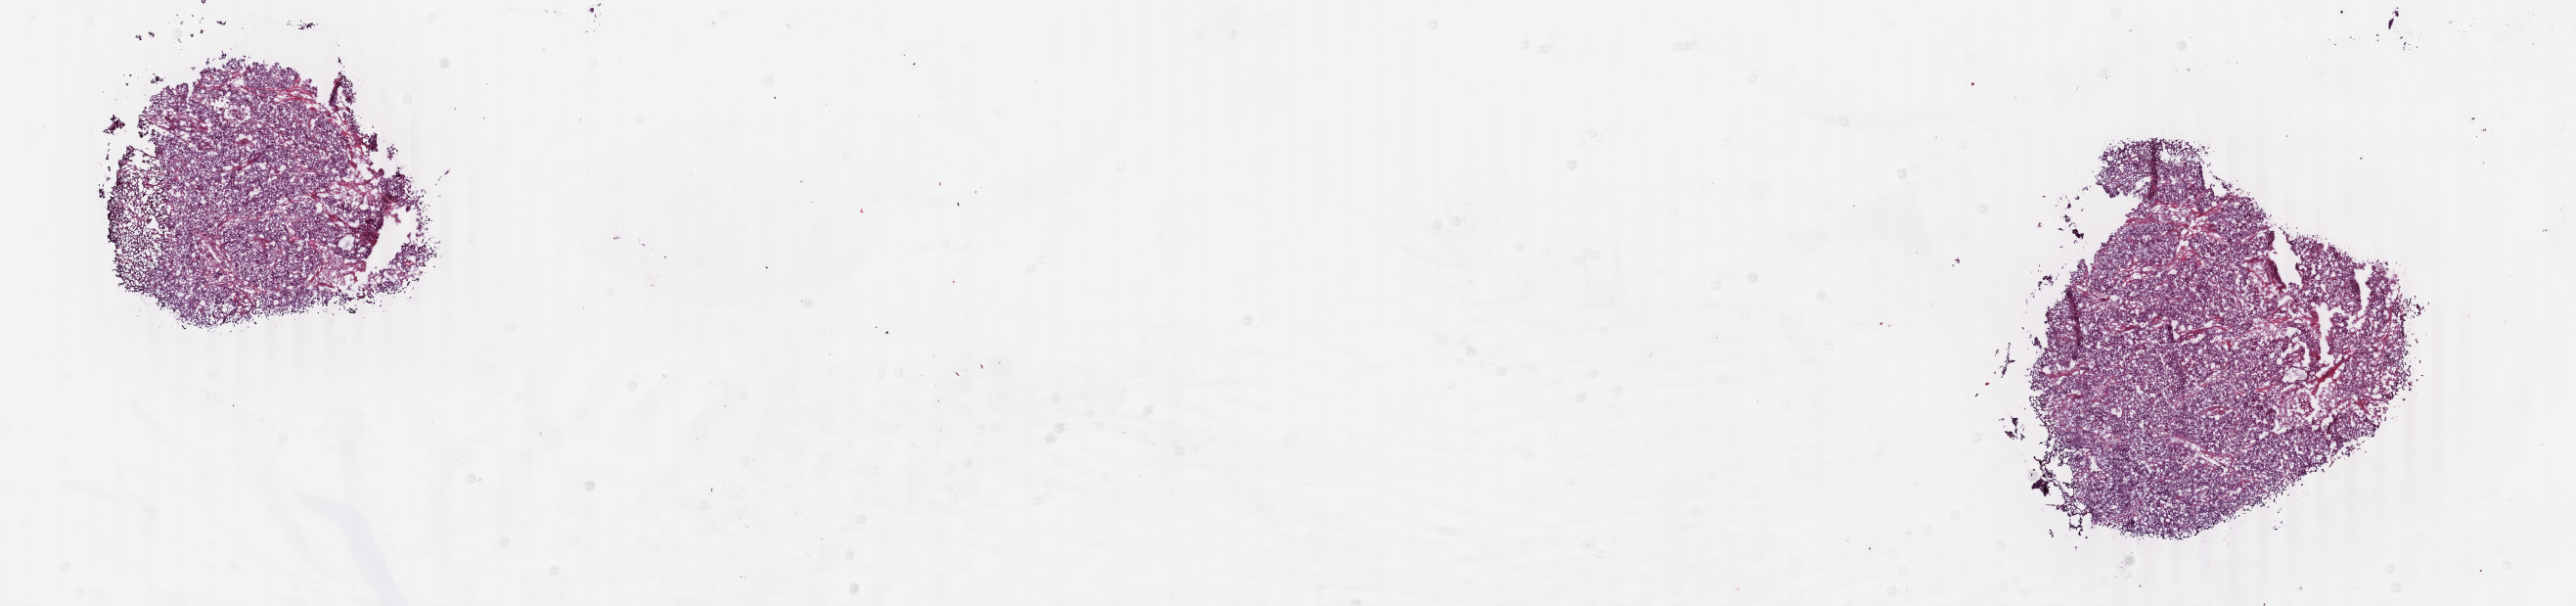
Whole-slide histology image, H&E-stained — low-resolution overview of the scanned area, about 20.9 x 4.9 mm, frozen section from the bottom of the tissue portion, sample: primary tumour, uterus. Female, age 59 years at initial diagnosis. Histologic grade: G3 (poorly differentiated). Composition of this section per pathologist review: tumour cells 85%, tumour nuclei 90%, normal cells 9%, stromal cells 1%, necrosis 5%. Infiltration values recorded for this section: lymphocyte infiltration 0%, monocyte infiltration 1%, neutrophil infiltration 0%.
Lymph nodes positive (case pathology): 2 of 16 examined. FIGO stage: IVA. Histologic diagnosis: Endometrioid adenocarcinoma, NOS (endometrium).